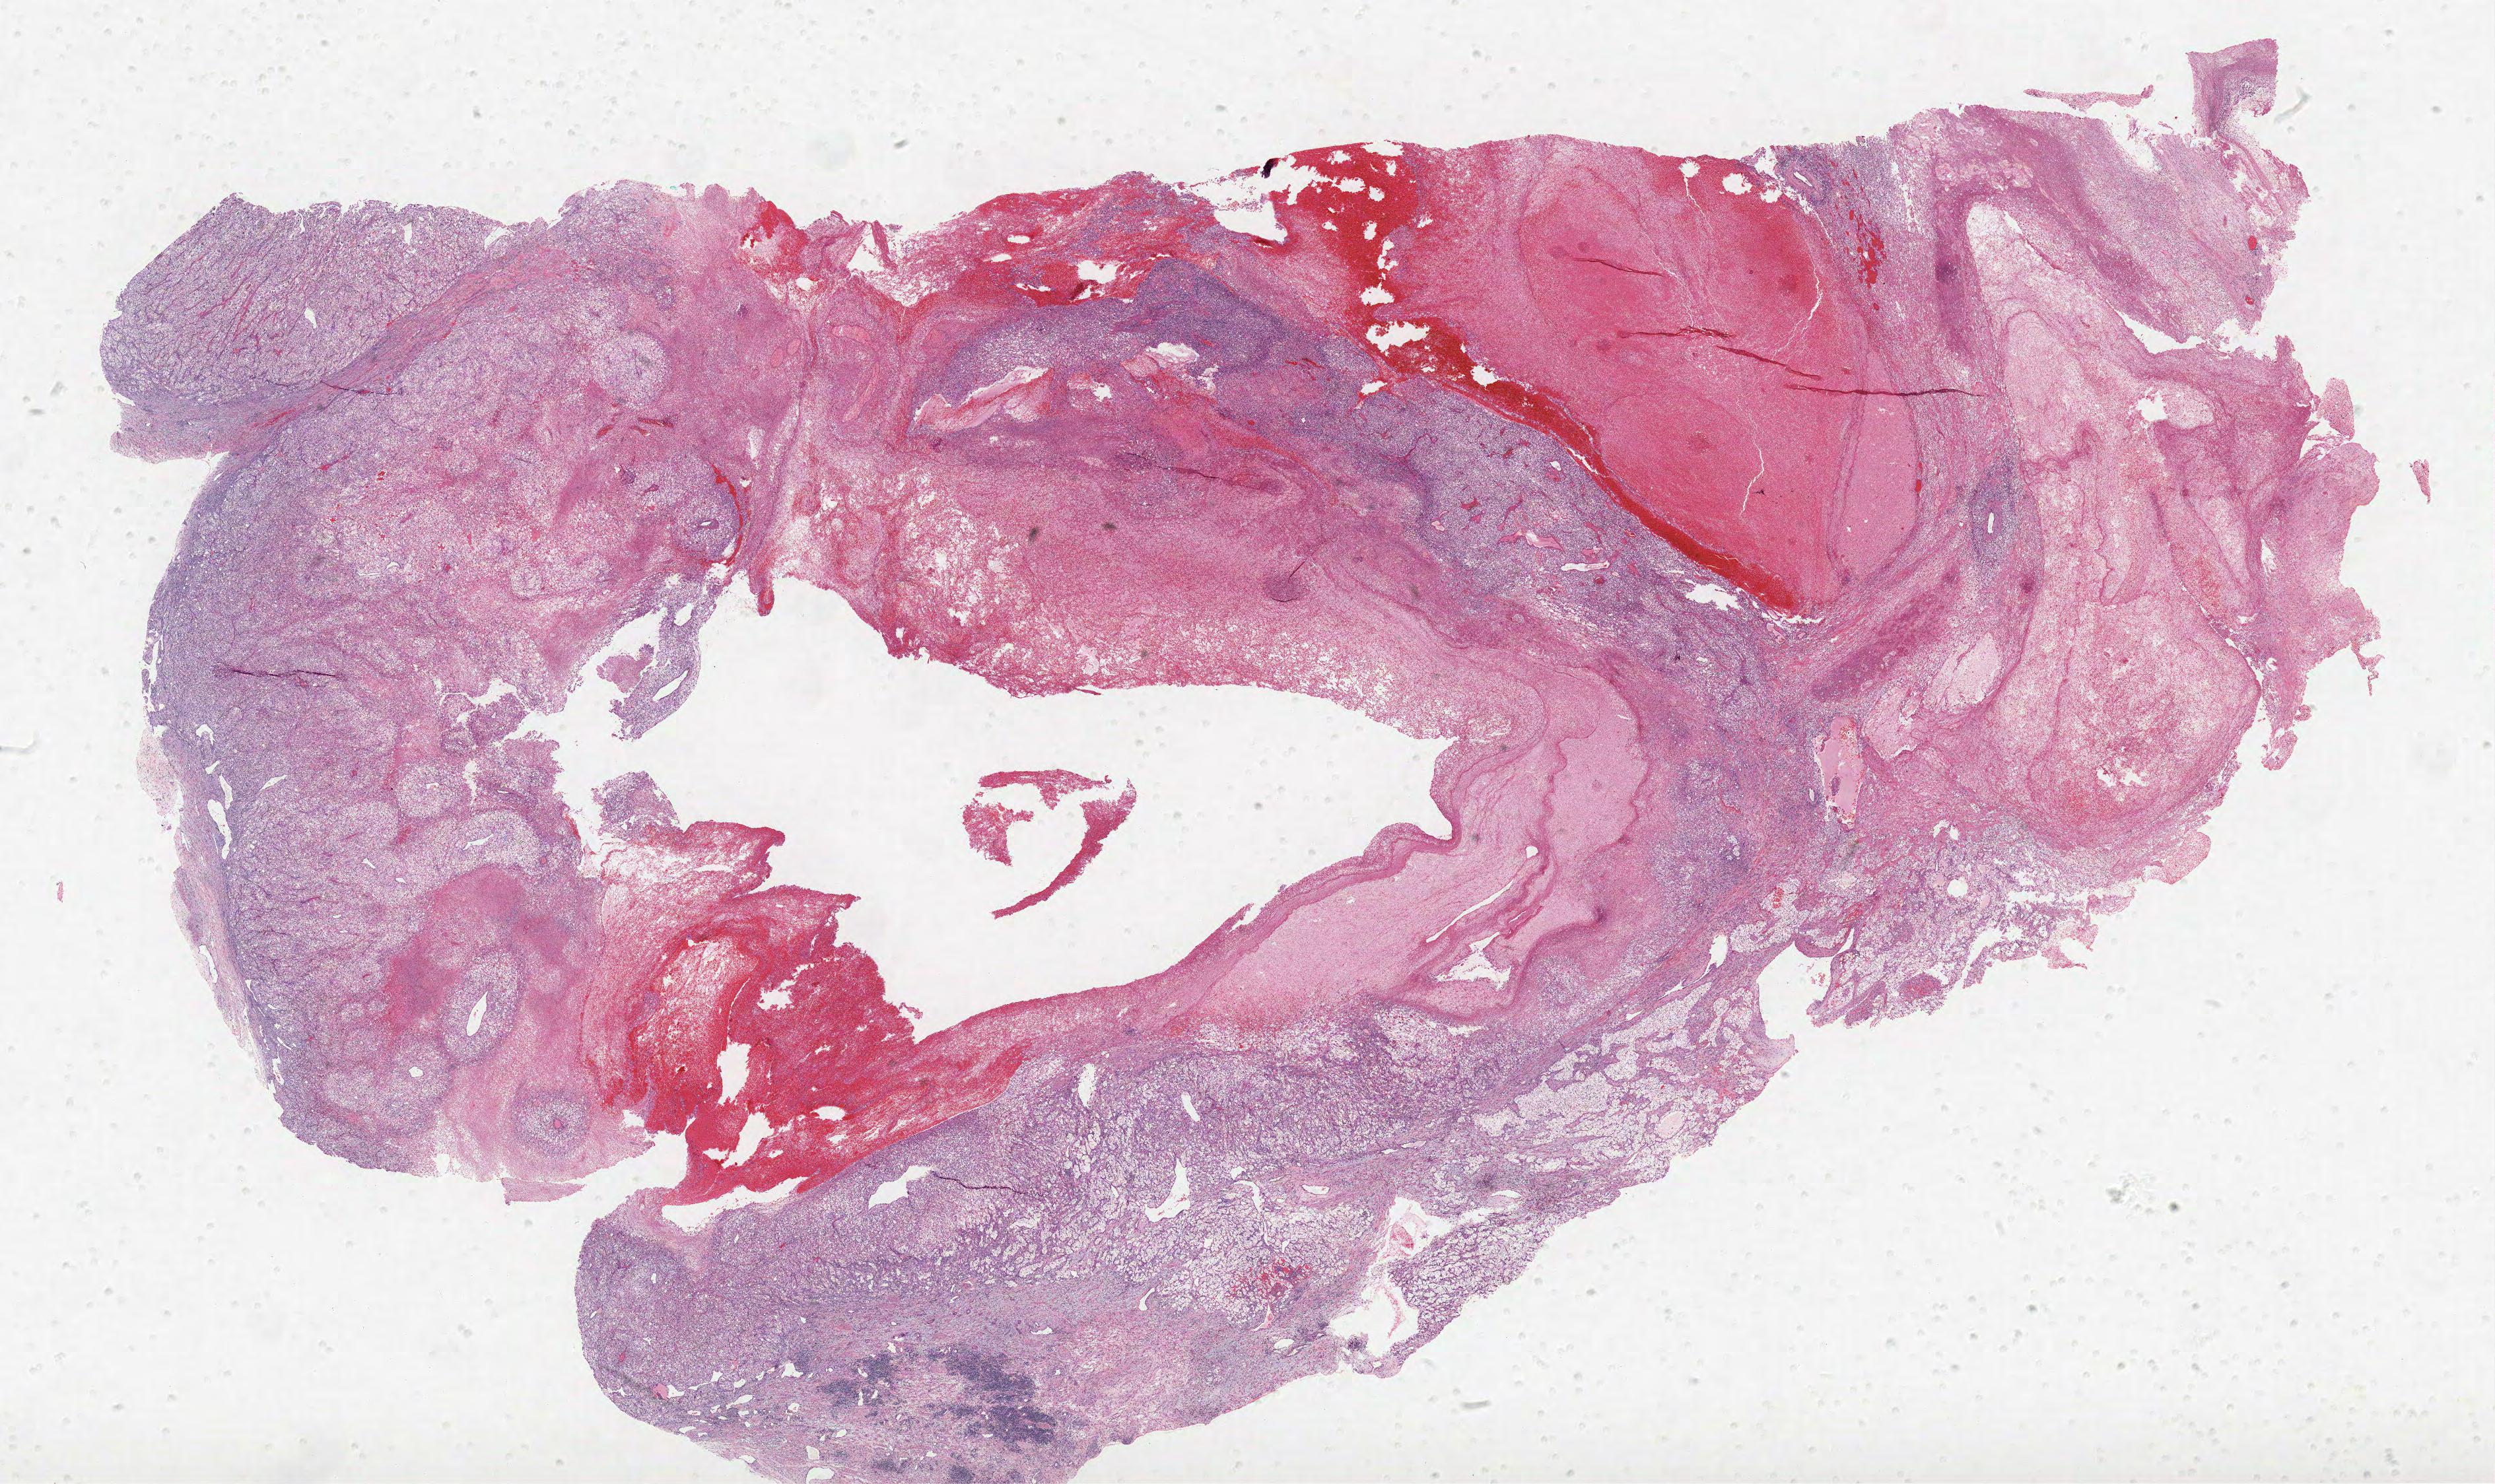
H&E-stained whole-slide image, shown as a low-resolution overview of the whole scanned area (about 30.2 x 18.0 mm). Formalin-fixed paraffin-embedded (FFPE) diagnostic section. Primary tumour sample from the kidney. Patient: male, age at initial diagnosis 79 years.
Histologic diagnosis: Clear cell adenocarcinoma, NOS.